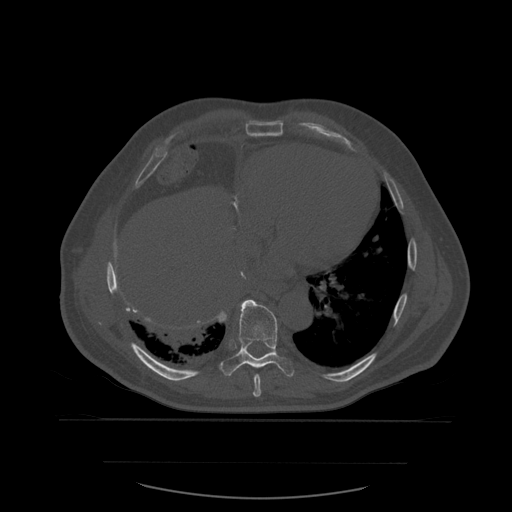
CT including the spine, one axial slice; slice 343 of 590 in the series (ordered by position); bone window (W 1800 / L 400 HU); 1.25 mm slice thickness; 512 × 512 image matrix. Patient age 71 years. From the clinical record (not read from this slice): primary cancer: lung; vertebrae with lytic lesions (as recorded): T1, T2, L5, S1.
Outlined on this slice (semi-automatic segmentation, software-assisted and operator-edited):
- T8 vertebra: bounding box (x1, y1, x2, y2) in pixels: (253, 374, 262, 397)
- T9 vertebra: (219, 300, 295, 377)